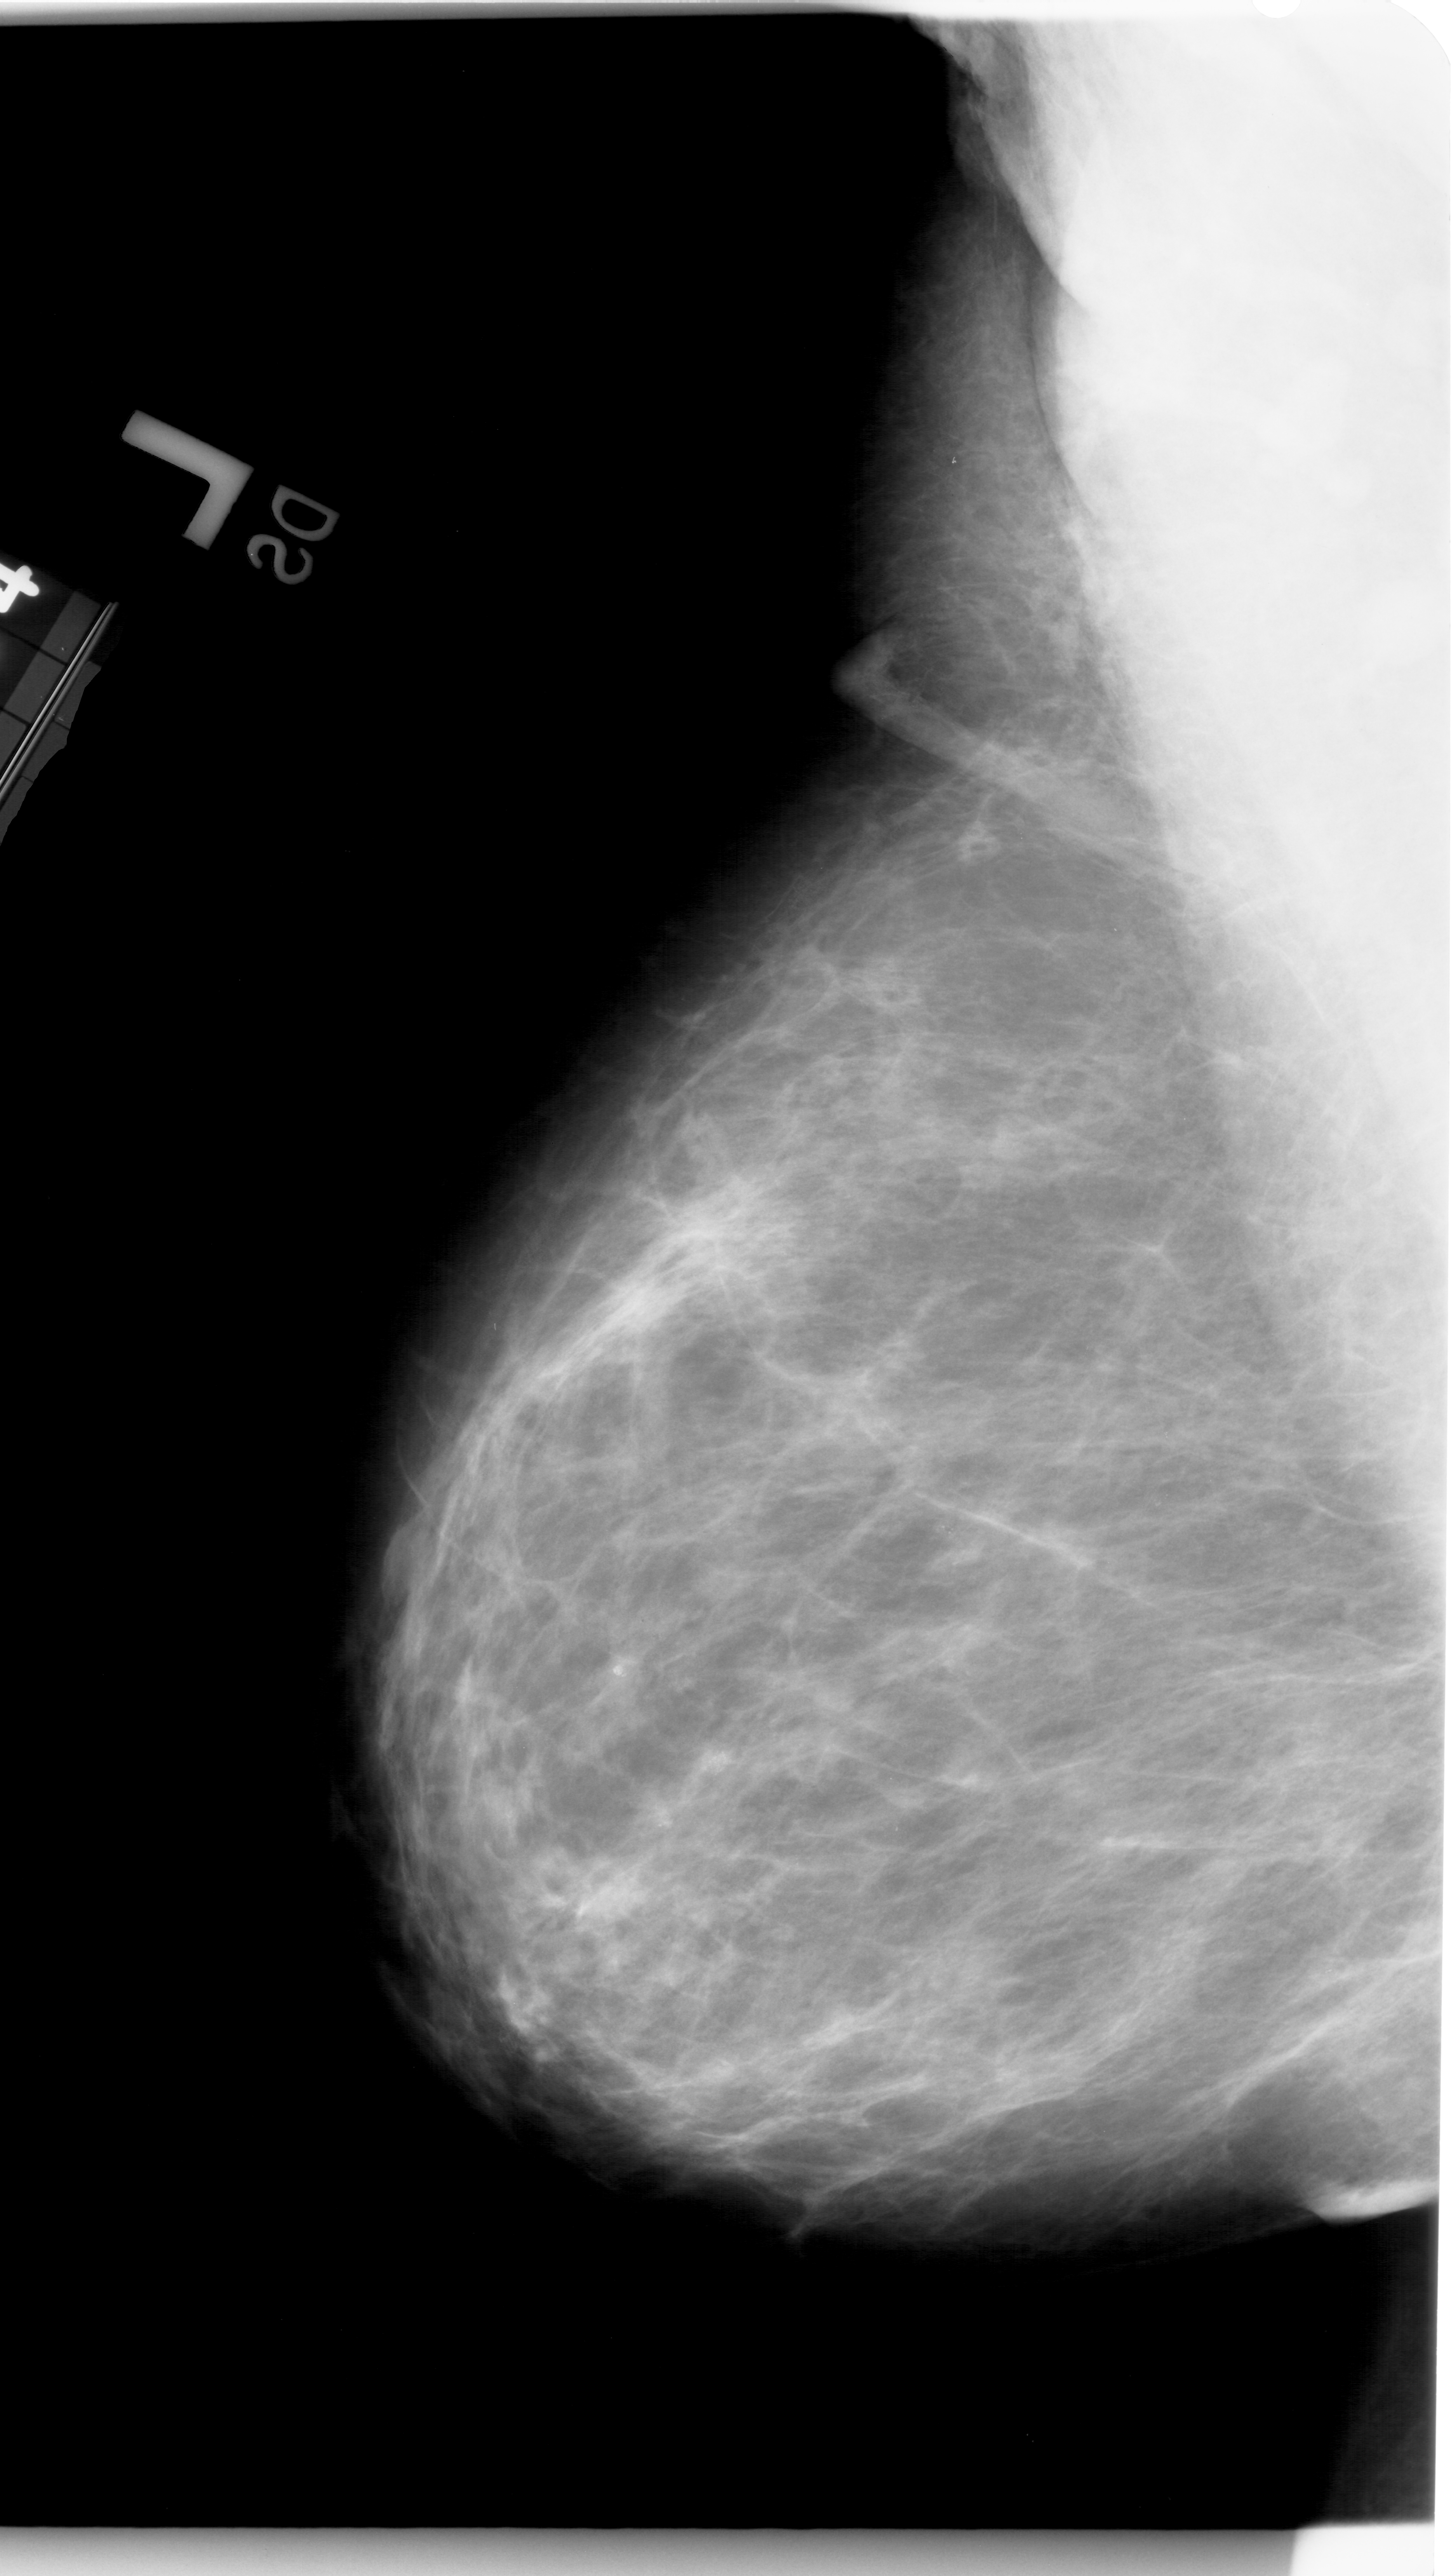
Digitized screen-film mammogram, left breast, mediolateral oblique (MLO) view, breast composition: heterogeneously dense (BI-RADS density category 3 of 4).
Marked findings (only marked abnormalities are described; nothing is implied about the rest of the image): calcifications, morphology pleomorphic, distribution clustered; BI-RADS assessment category 4; subtlety rating 2 on a 1 (subtle) to 5 (obvious) scale; pathology (as recorded): malignant.